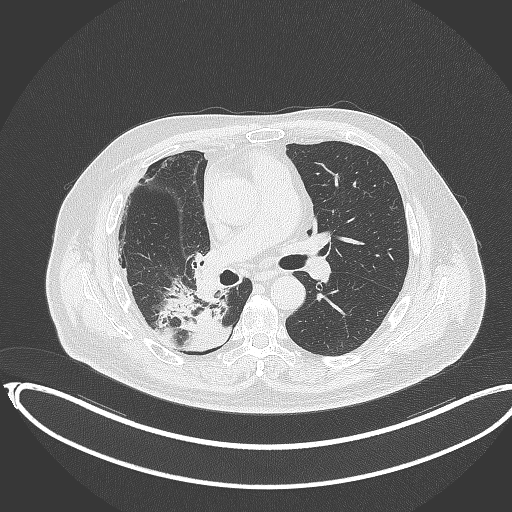
Chest CT, one axial slice. Slice 197 of 403 in the series (ordered by position). Lung window (W 1500 / L -600 HU). 1 mm slice thickness. 512 × 512 image matrix, field of view 436 × 436 mm. Patient: male, 68 years. Case-level facts recorded for this patient, not image findings: clinical TNM (as recorded): T2a N0 M0.
Structures marked on this image (rectangle marked by the reading radiologist):
- lung tumour (recorded histology: adenocarcinoma): bounding box [x1, y1, x2, y2] px = [145, 296, 236, 356]